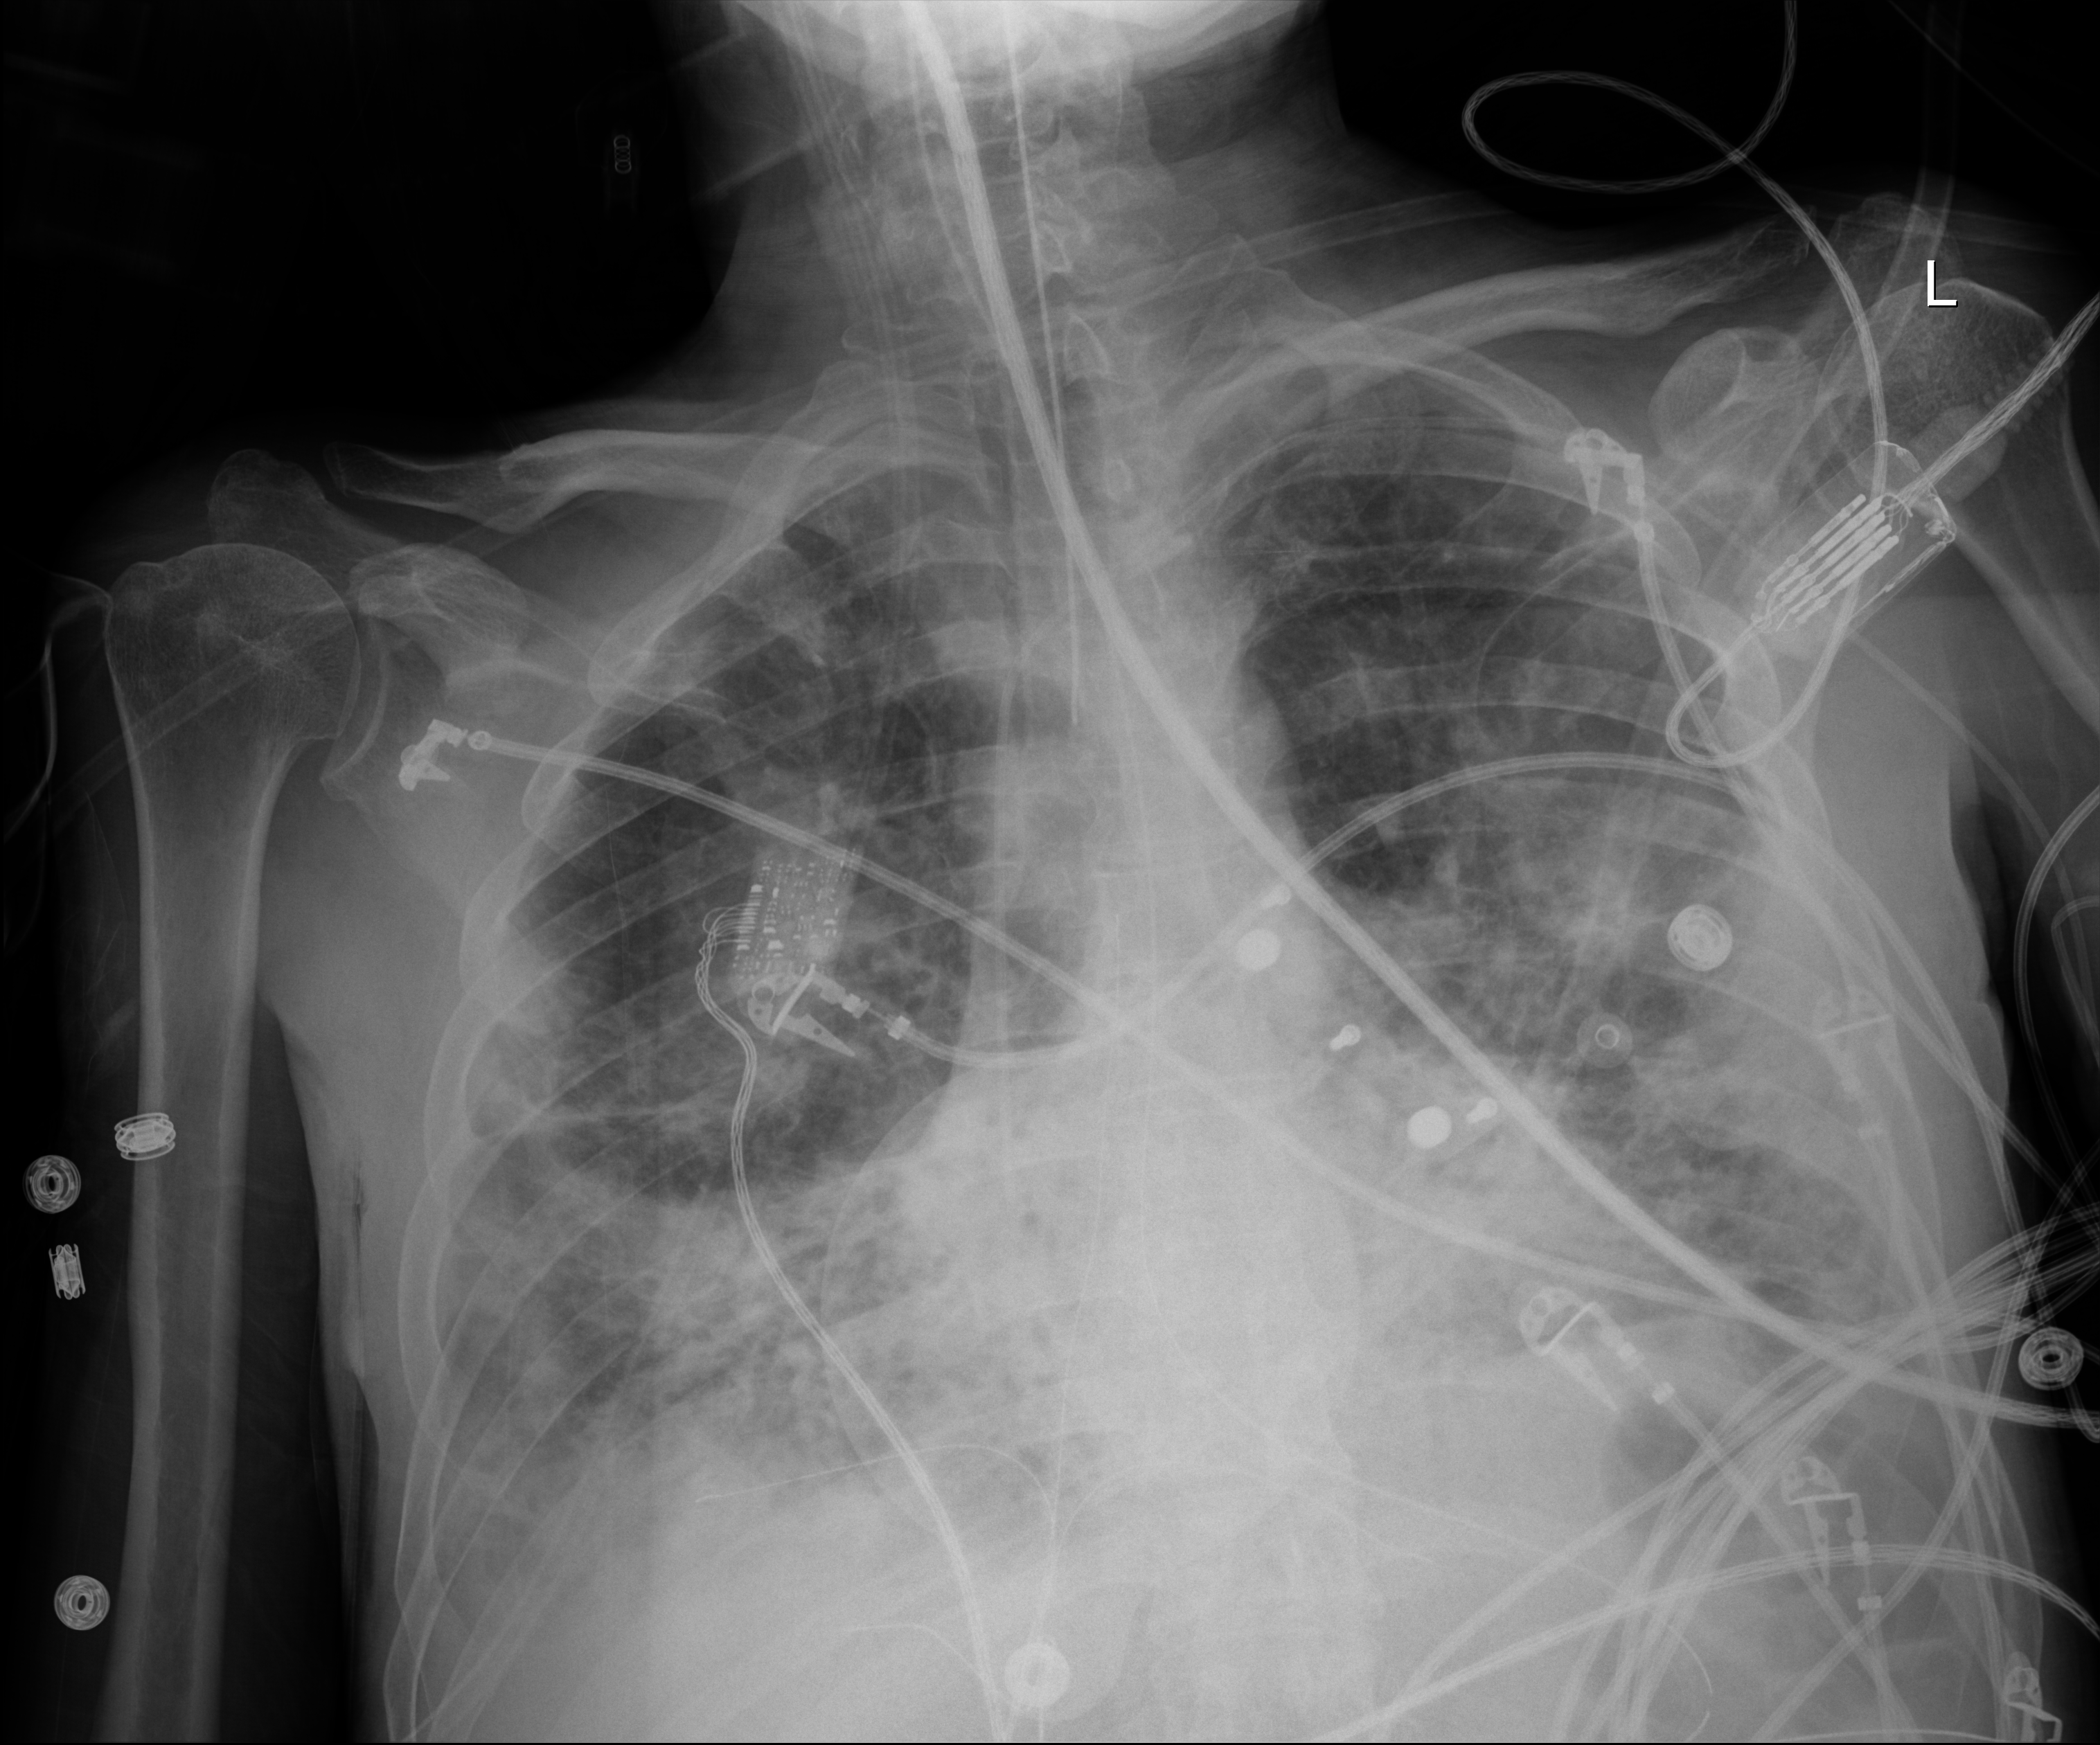
Portable chest radiograph. Male patient hospitalised with COVID-19, age 18–59 years.
Admission-level facts for this patient (not findings on this image; timing relative to this image not recorded):
- admitted to intensive care during this hospital stay: yes
- chronic kidney disease (admission record): no